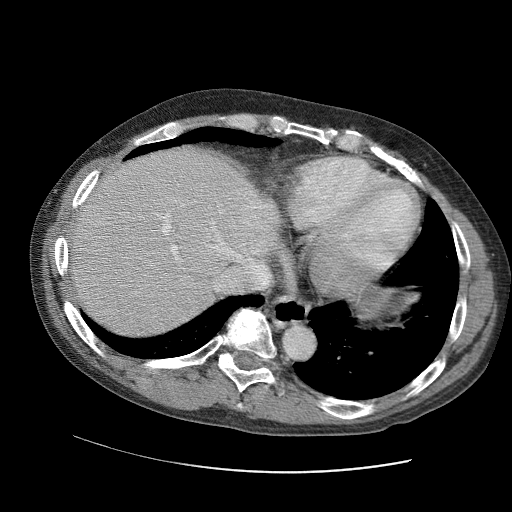
Contrast-enhanced abdominal CT (liver protocol), one axial slice. Slice 84 of 109 in the series (ordered by position). Reconstruction kernel STANDARD. Soft-tissue window (W 400 / L 40 HU). 2.5 mm slice thickness. 512 × 512 image matrix, field of view 400 × 400 mm. Case-level facts recorded for this patient, not image findings: diagnosis: hepatocellular carcinoma (patient treated with transarterial chemoembolisation; whether this scan precedes or follows treatment is not stated here); TNM stage (as recorded): Stage-IIIC; Child-Pugh class: B; tumour differentiation: well differentiated; tumour nodularity: uninodular.
Annotated regions visible in this slice (semi-automatic segmentation, software-assisted and operator-edited):
- abdominal aorta: box from (x=284, y=324) to (x=314, y=356) px
- liver parenchyma outside the tumour (the mass and vessels are separate outlines, so this box may not span the whole liver): (x=64, y=146)–(x=278, y=336)
- liver vessels: (x=123, y=204)–(x=265, y=283)